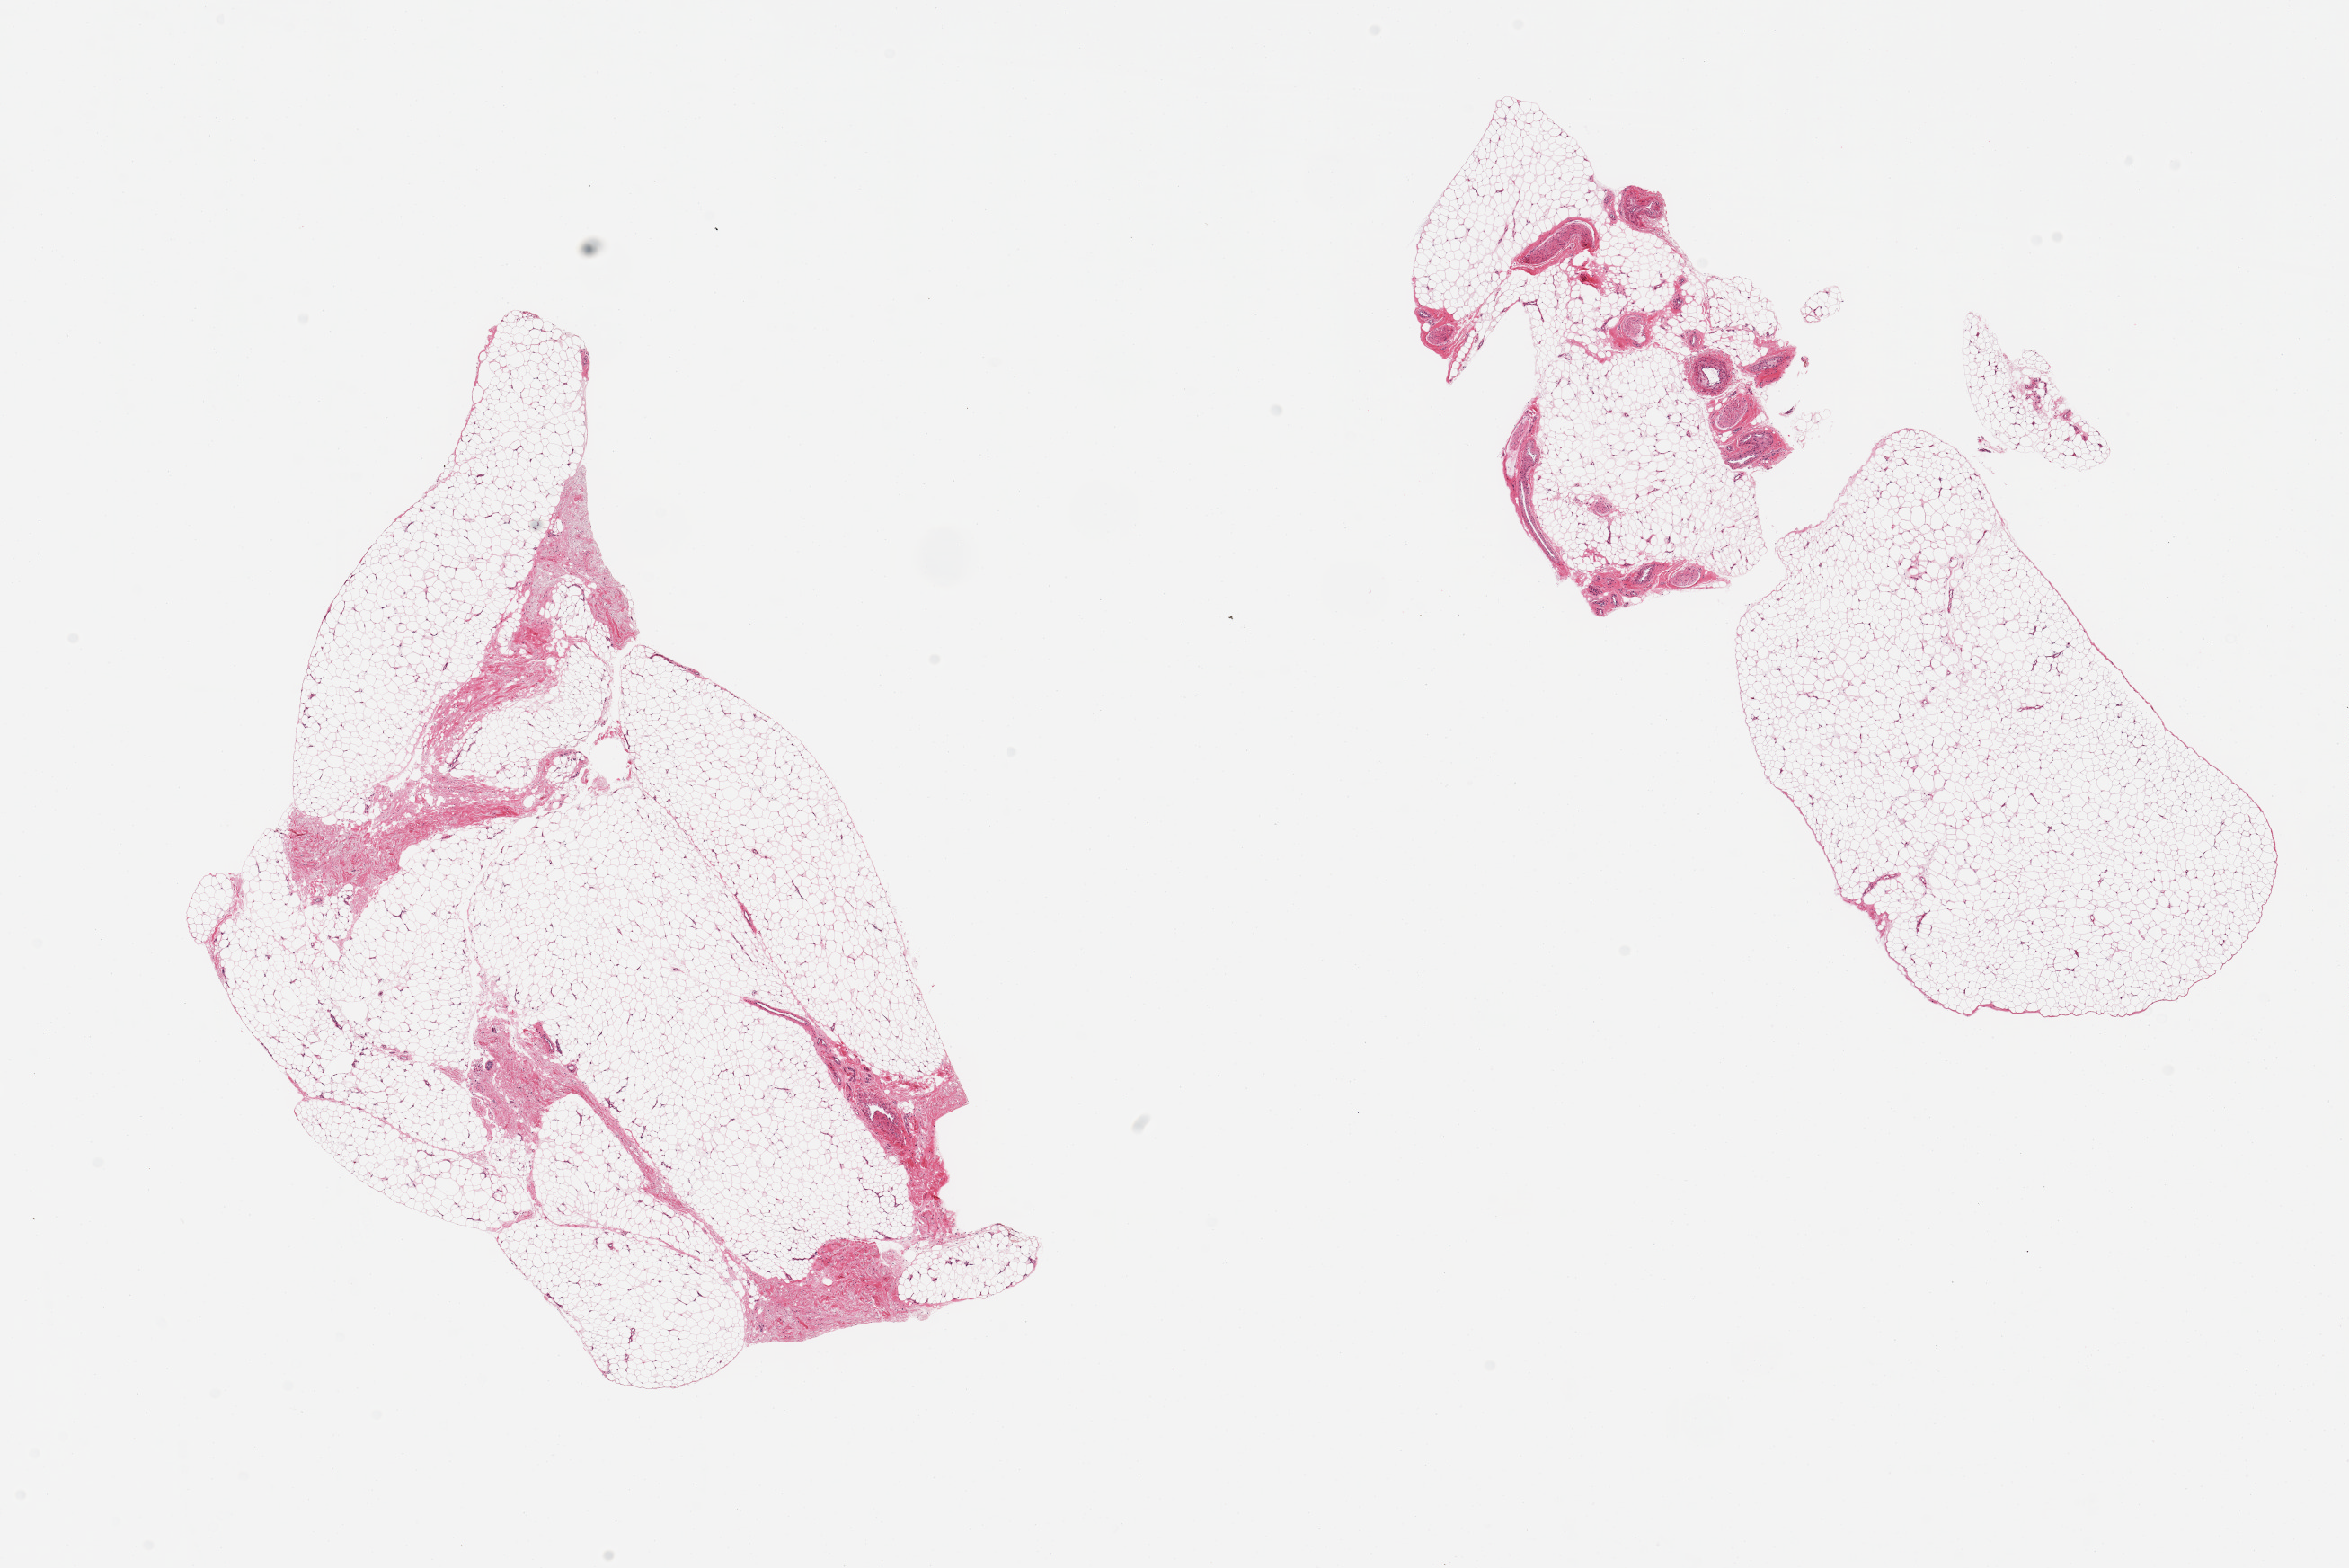
Digitized hematoxylin and eosin (H&E)-stained section, brightfield — a low-resolution overview of the entire scanned area, about 20.7 x 13.8 mm (slide scanned at 20x); PAXgene-fixed, paraffin-embedded tissue; sampled site (target tissue): adipose tissue; donor tissue sample. Donor sex: male.
Review note (as recorded): 2 pieces, ~10% fascia/vascular elements.